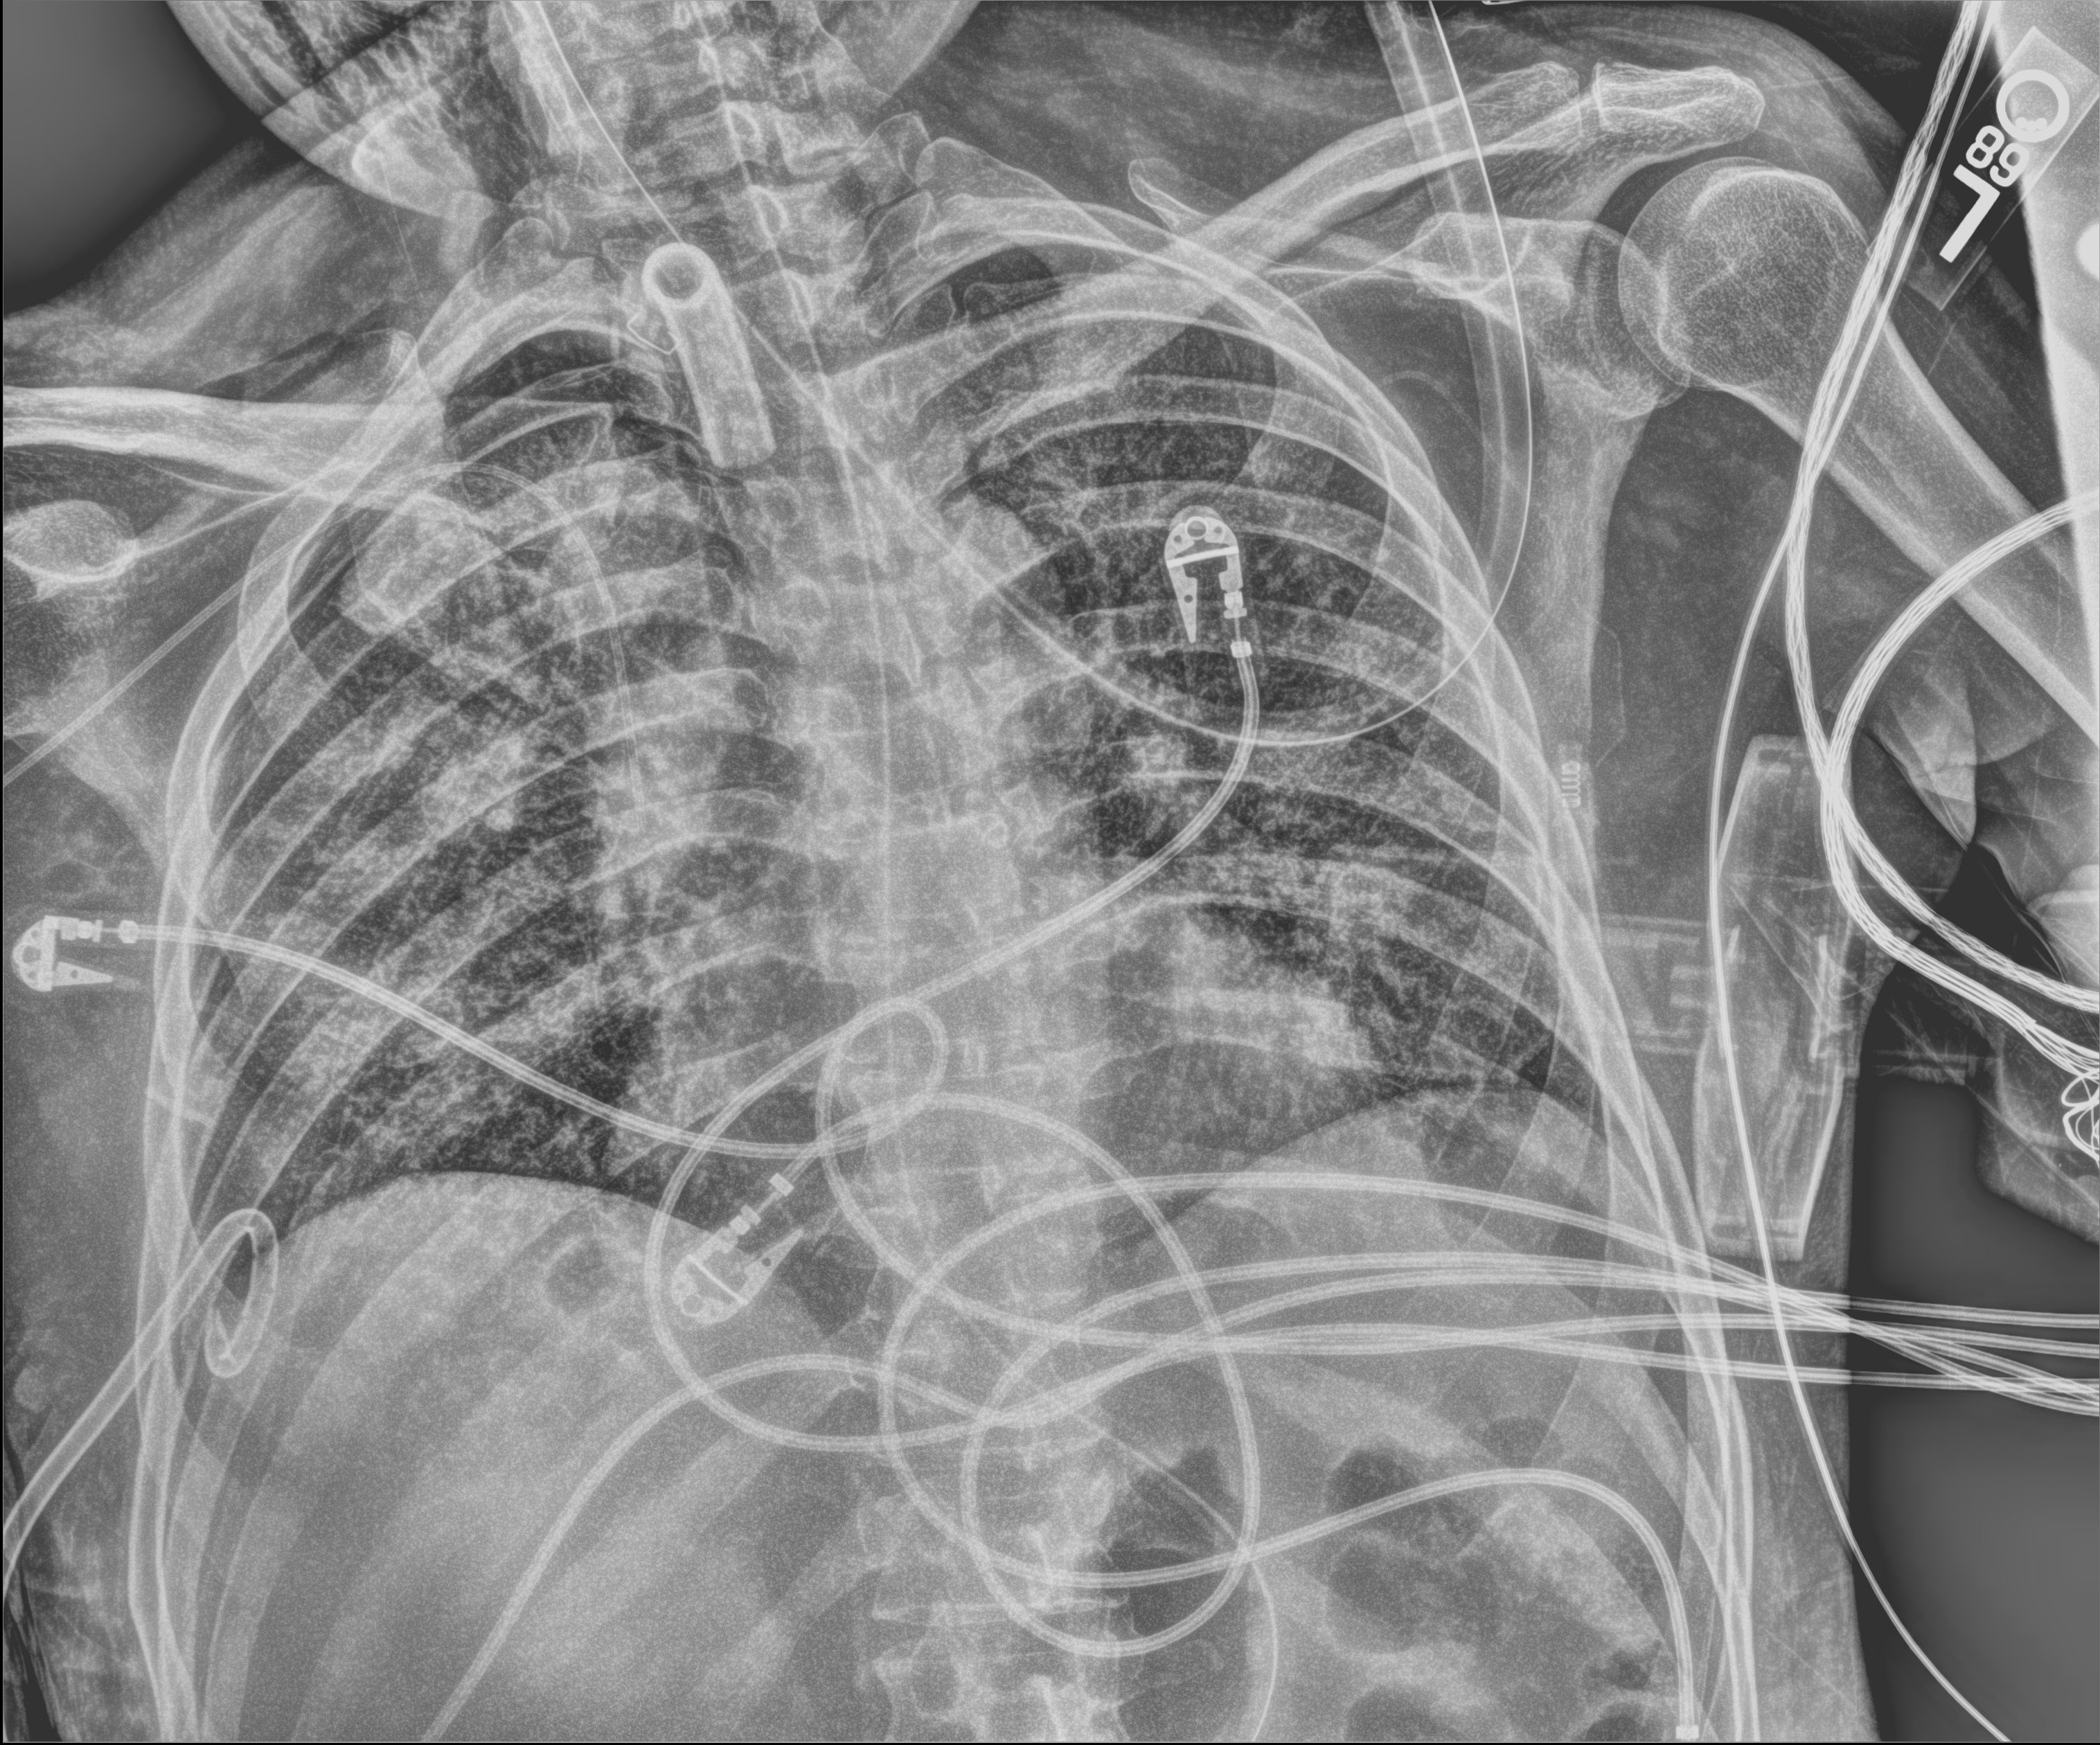
Chest X-ray (portable), anteroposterior (AP) projection. Male patient hospitalised with COVID-19, age 18–59 years.
From the hospital-stay record, not from the radiograph (when in the stay this image was taken is not recorded): length of hospital stay: 77 days; other chronic lung disease (admission record): no.